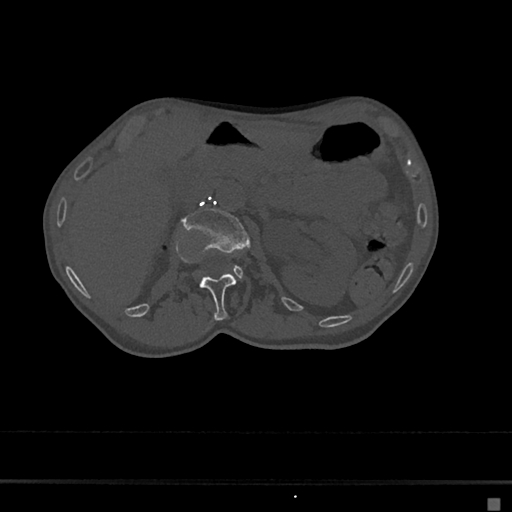
CT including the spine, one axial slice; slice 53 of 797 in the series (ordered by position); 120 kVp; bone window (W 1800 / L 400 HU); 0.5 mm slice thickness; 512 × 512 image matrix. Female patient, age 68 years. Case-level facts recorded for this patient, not image findings: primary cancer: renal.
Outlined on this slice (semi-automatic segmentation, software-assisted and operator-edited):
- L1 vertebra: box from (x=199, y=273) to (x=236, y=321) px
- L2 vertebra: (x=184, y=207)–(x=249, y=276)